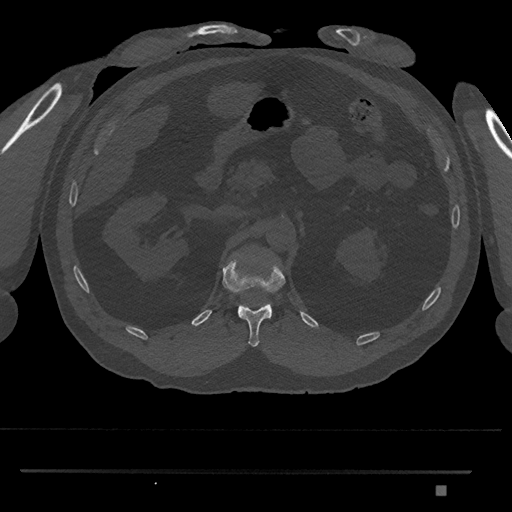
CT including the spine, one axial slice. Position 870 of 1134 along the scan axis. 120 kVp. Bone window (W 1800 / L 400 HU). 0.5 mm slice thickness. 512 × 512 image matrix, field of view 429 × 429 mm. Patient: male, 65 years. From the clinical record (not read from this slice): primary cancer: prostate.
Structures marked on this image (semi-automatic segmentation, software-assisted and operator-edited):
- L1 vertebra: bounding box (x1, y1, x2, y2) in pixels: (270, 305, 273, 318)
- T12 vertebra: (222, 259, 286, 347)